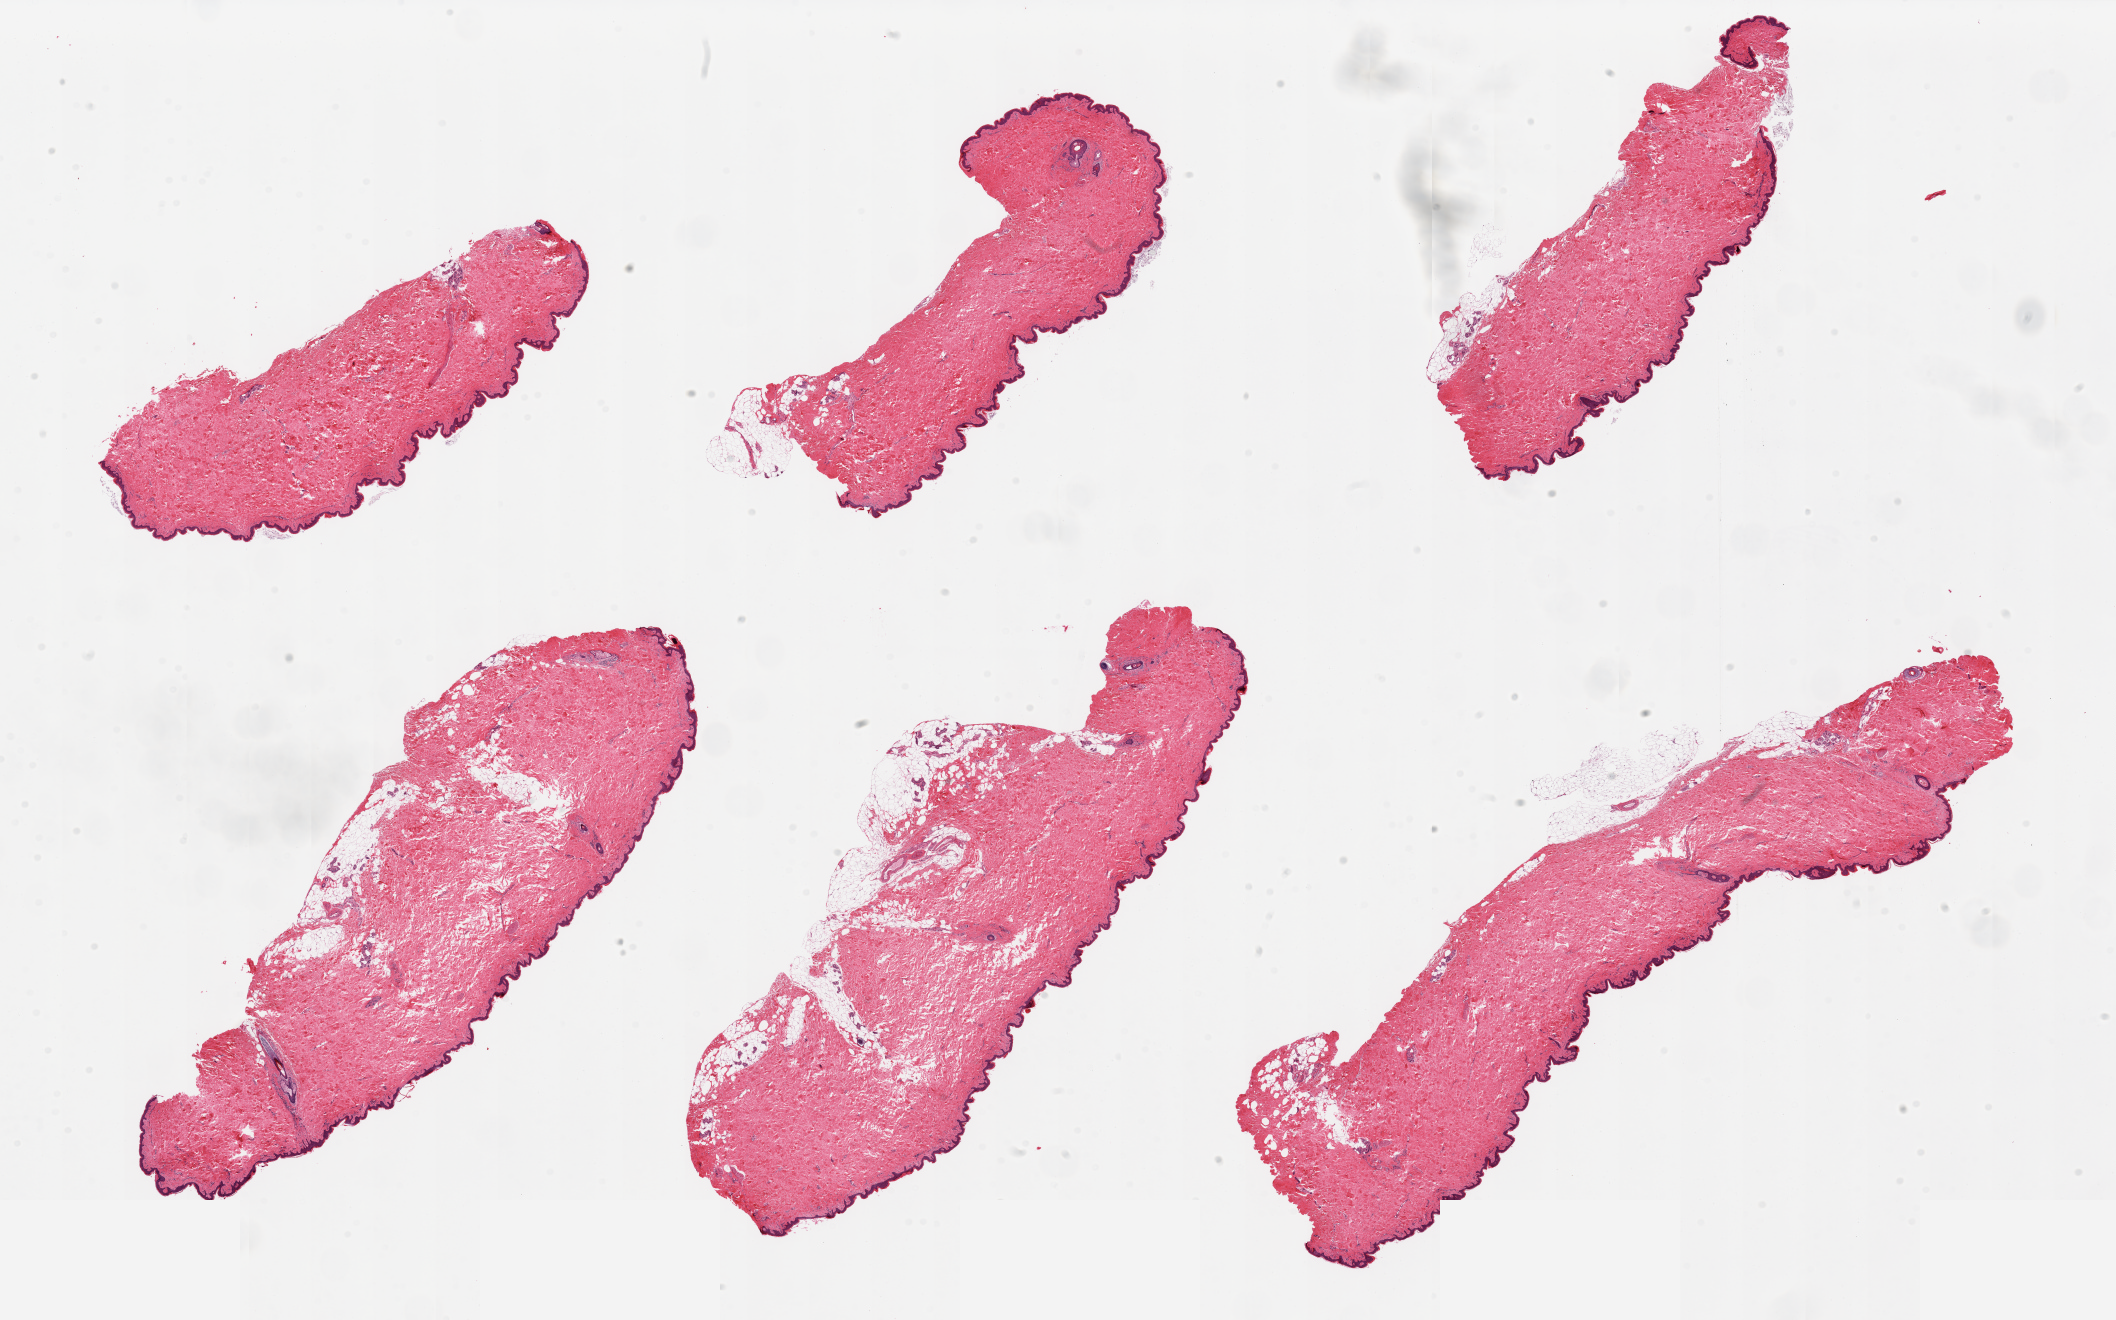
Haematoxylin and eosin whole-slide image, shown as a low-resolution overview of the whole scanned area (about 33.5 x 20.9 mm, from a 20x scan); PAXgene-fixed, paraffin-embedded tissue; section of skin of suprapubic region (target tissue); donor tissue sample. Donor sex: female.
• review note (as recorded): 6 pieces, well trimmed